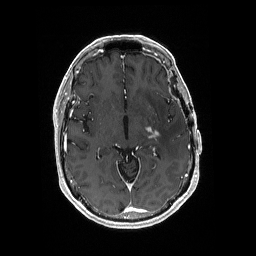
Brain MRI from a brain-tumour surgery series, one axial slice; slice 105 of 176 in the series (ordered by position); T1-weighted post-contrast; 1 mm slice thickness; 256 × 256 image matrix, field of view 256 × 256 mm. From the clinical record (not read from this slice): histopathology: Glioblastoma; WHO grade: 4; IDH mutation: no; tumour location: Left Medial Temporal.
Outlined on this slice (manually delineated by an expert):
- tumour: bounding box <144,125,160,139> (left, top, right, bottom; pixels)